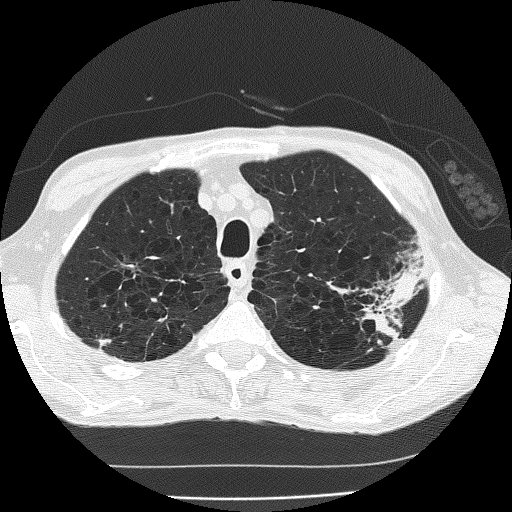
Low-dose screening chest CT, one axial slice; slice 149 of 185 in the series (ordered by position); reconstruction kernel FC51; 120 kVp; lung window (W 1500 / L -600 HU); 512 × 512 image matrix.
Outlined on this slice (outlined manually by an expert reader):
- lesion 1 (tumor, upper lobe of left lung): bounding box [x1, y1, x2, y2] px = [364, 267, 421, 337]